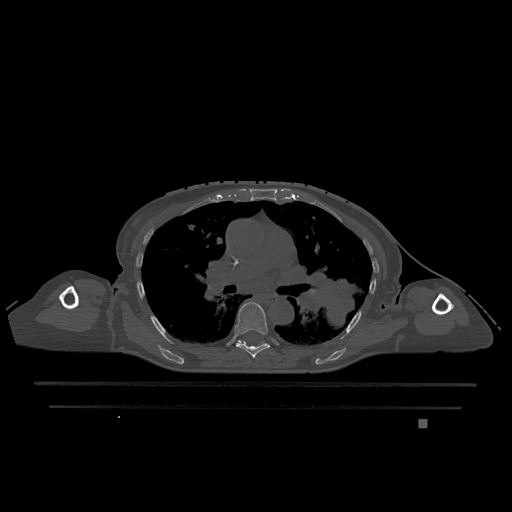
CT including the spine, one axial slice. Position 781 of 1317 along the scan axis. Bone window (W 1800 / L 400 HU). 512 × 512 image matrix. Patient: female, 74 years. From the clinical record (not read from this slice): primary cancer: lung; vertebrae with lytic lesions (as recorded): T1, T4, T5, T6, L4, L5.
Annotated regions visible in this slice (semi-automatic segmentation, software-assisted and operator-edited):
- T6 vertebra: bounding box [x1, y1, x2, y2] px = [235, 302, 270, 358]
- T7 vertebra: [238, 340, 264, 343]